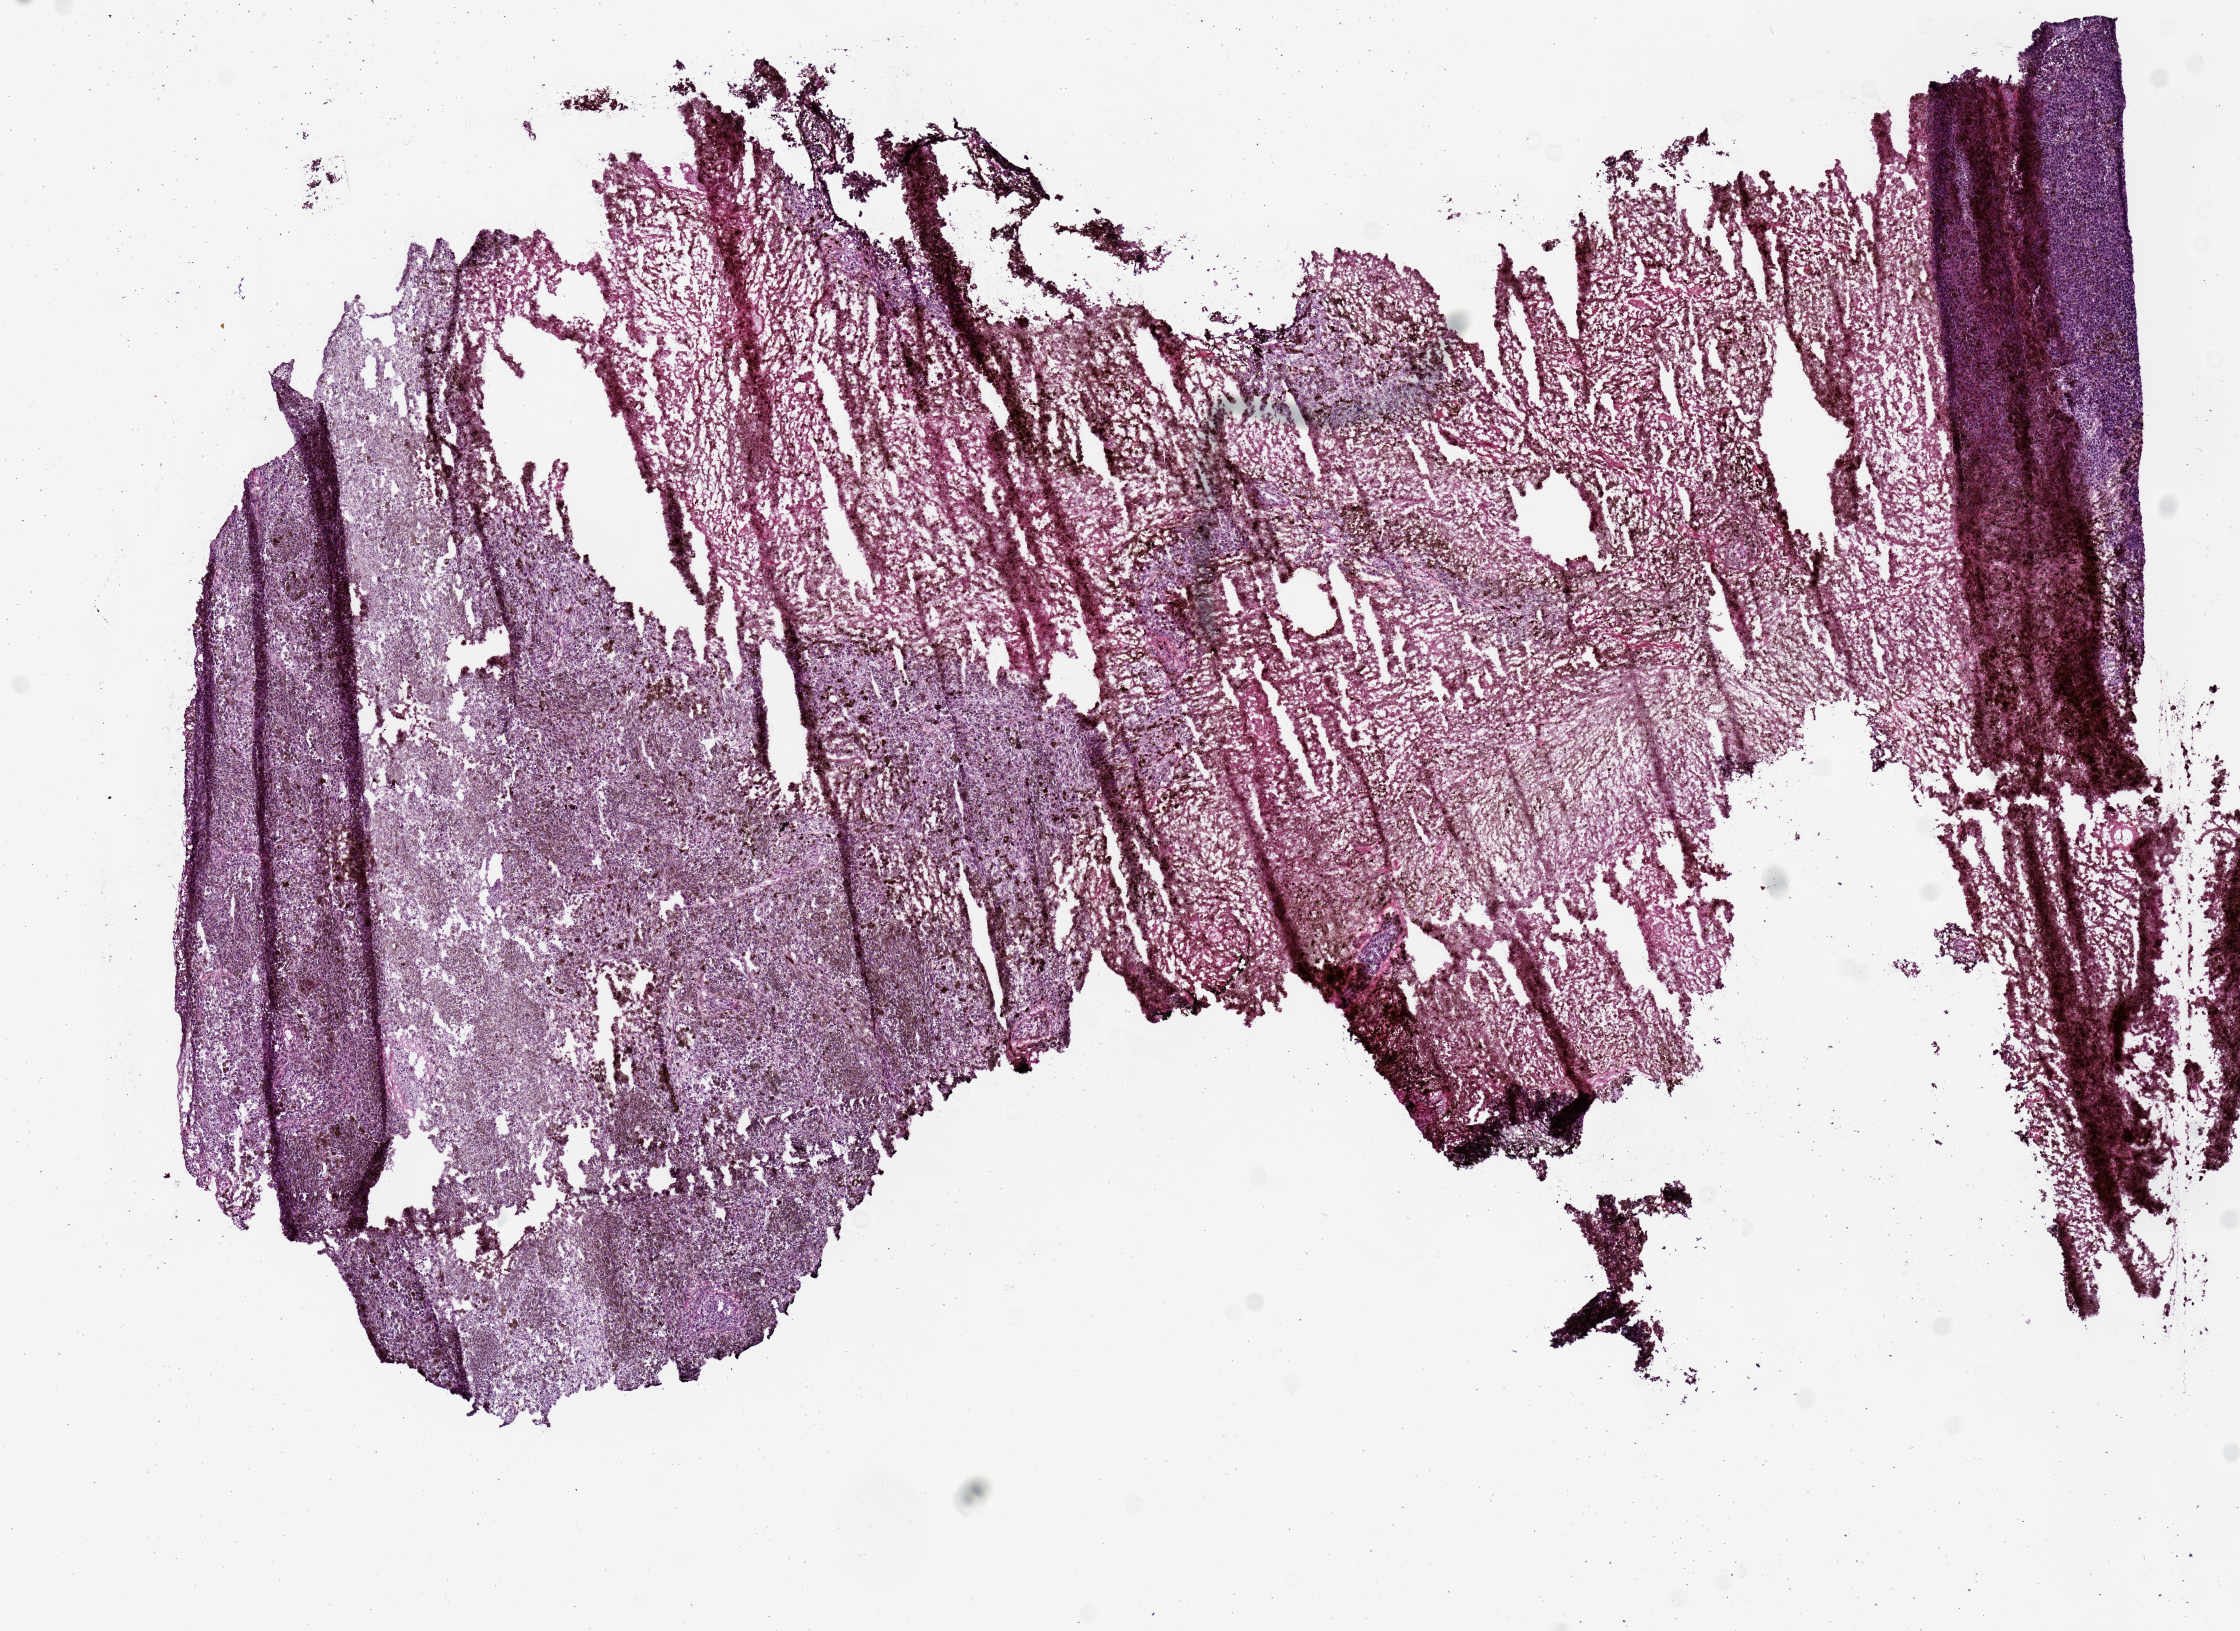
Whole-slide histology image, H&E-stained, shown as a low-resolution overview of the whole scanned area (about 8.9 x 6.4 mm, slide scanned at 20x); frozen section from the top of the tissue portion; metastatic tumour sample, sampled site: upper lobe, lung. Patient: female, age at initial diagnosis 72 years.
This section: metastatic tumour tissue. Patient diagnosis: Malignant melanoma, NOS.